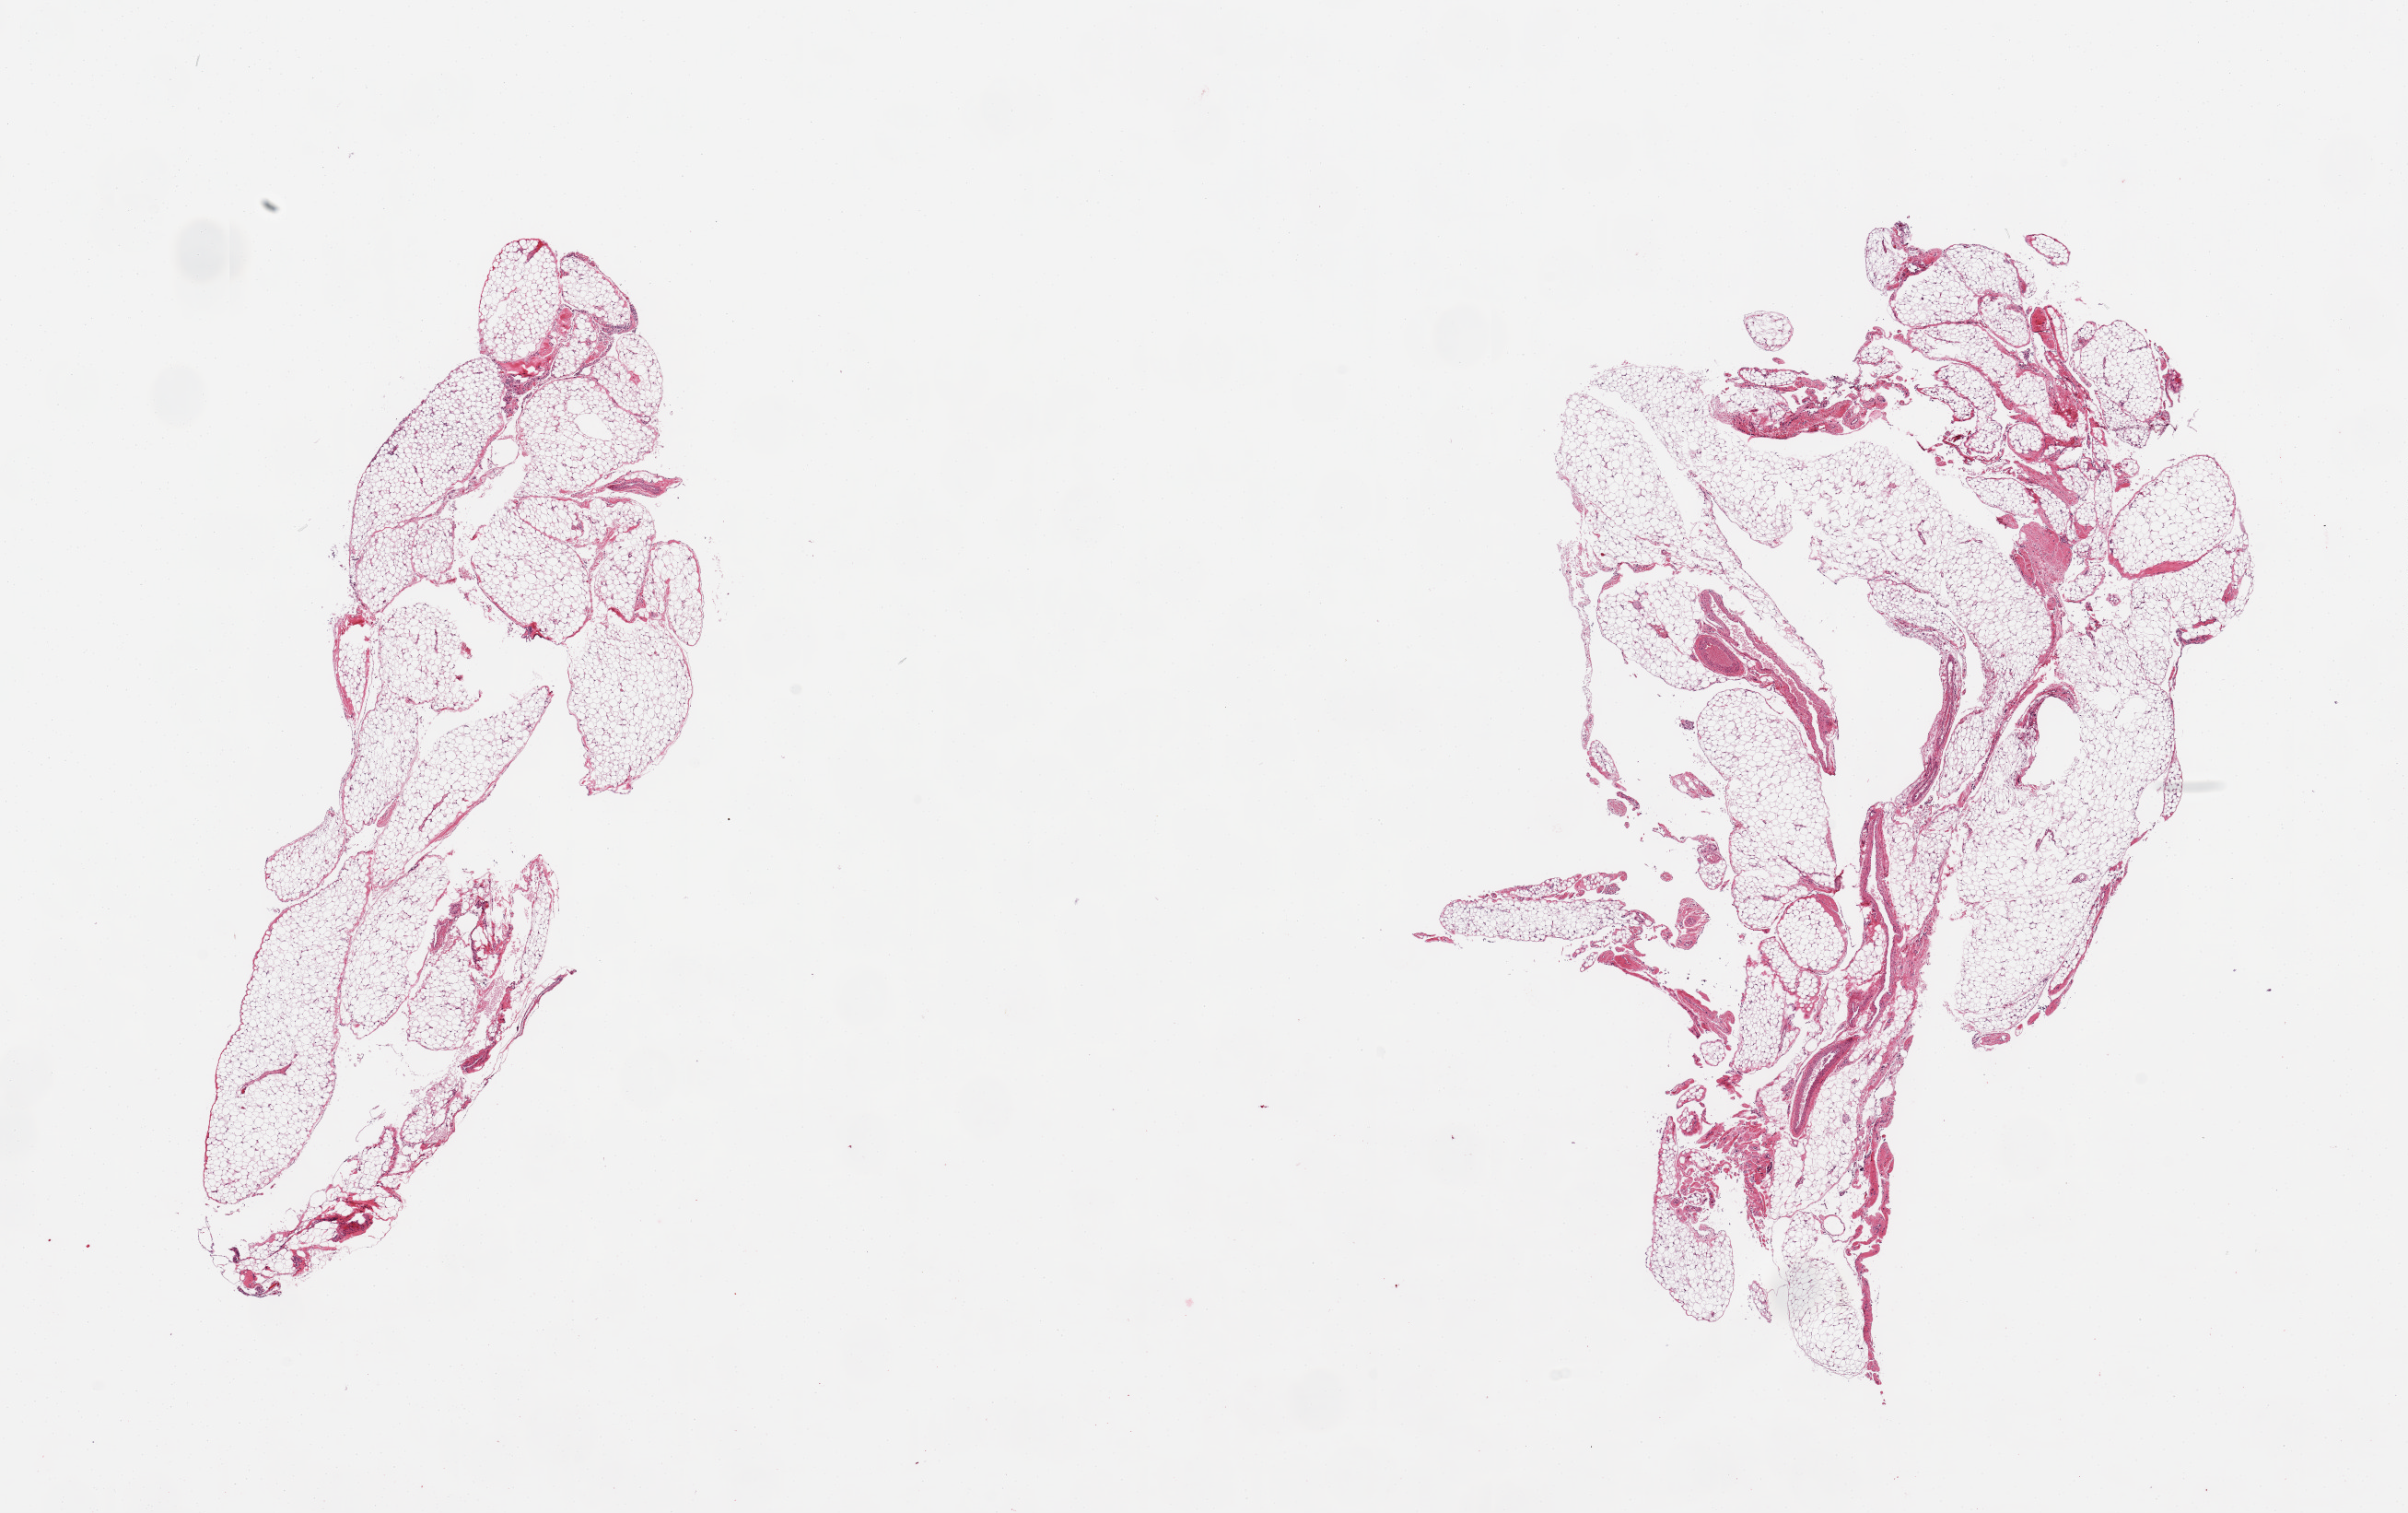
Whole-slide image, hematoxylin and eosin (H&E) stain, brightfield, a low-resolution overview of the entire scanned area, about 20.7 x 13.0 mm (acquisition: 20x scan). PAXgene-fixed paraffin-embedded (PFPE) section. Section of omentum (target tissue). Donor tissue sample. Female donor.
Review note (as recorded): 2 pieces, ~150-20% vascular elements/fascia/mesothelial hyperplasia.